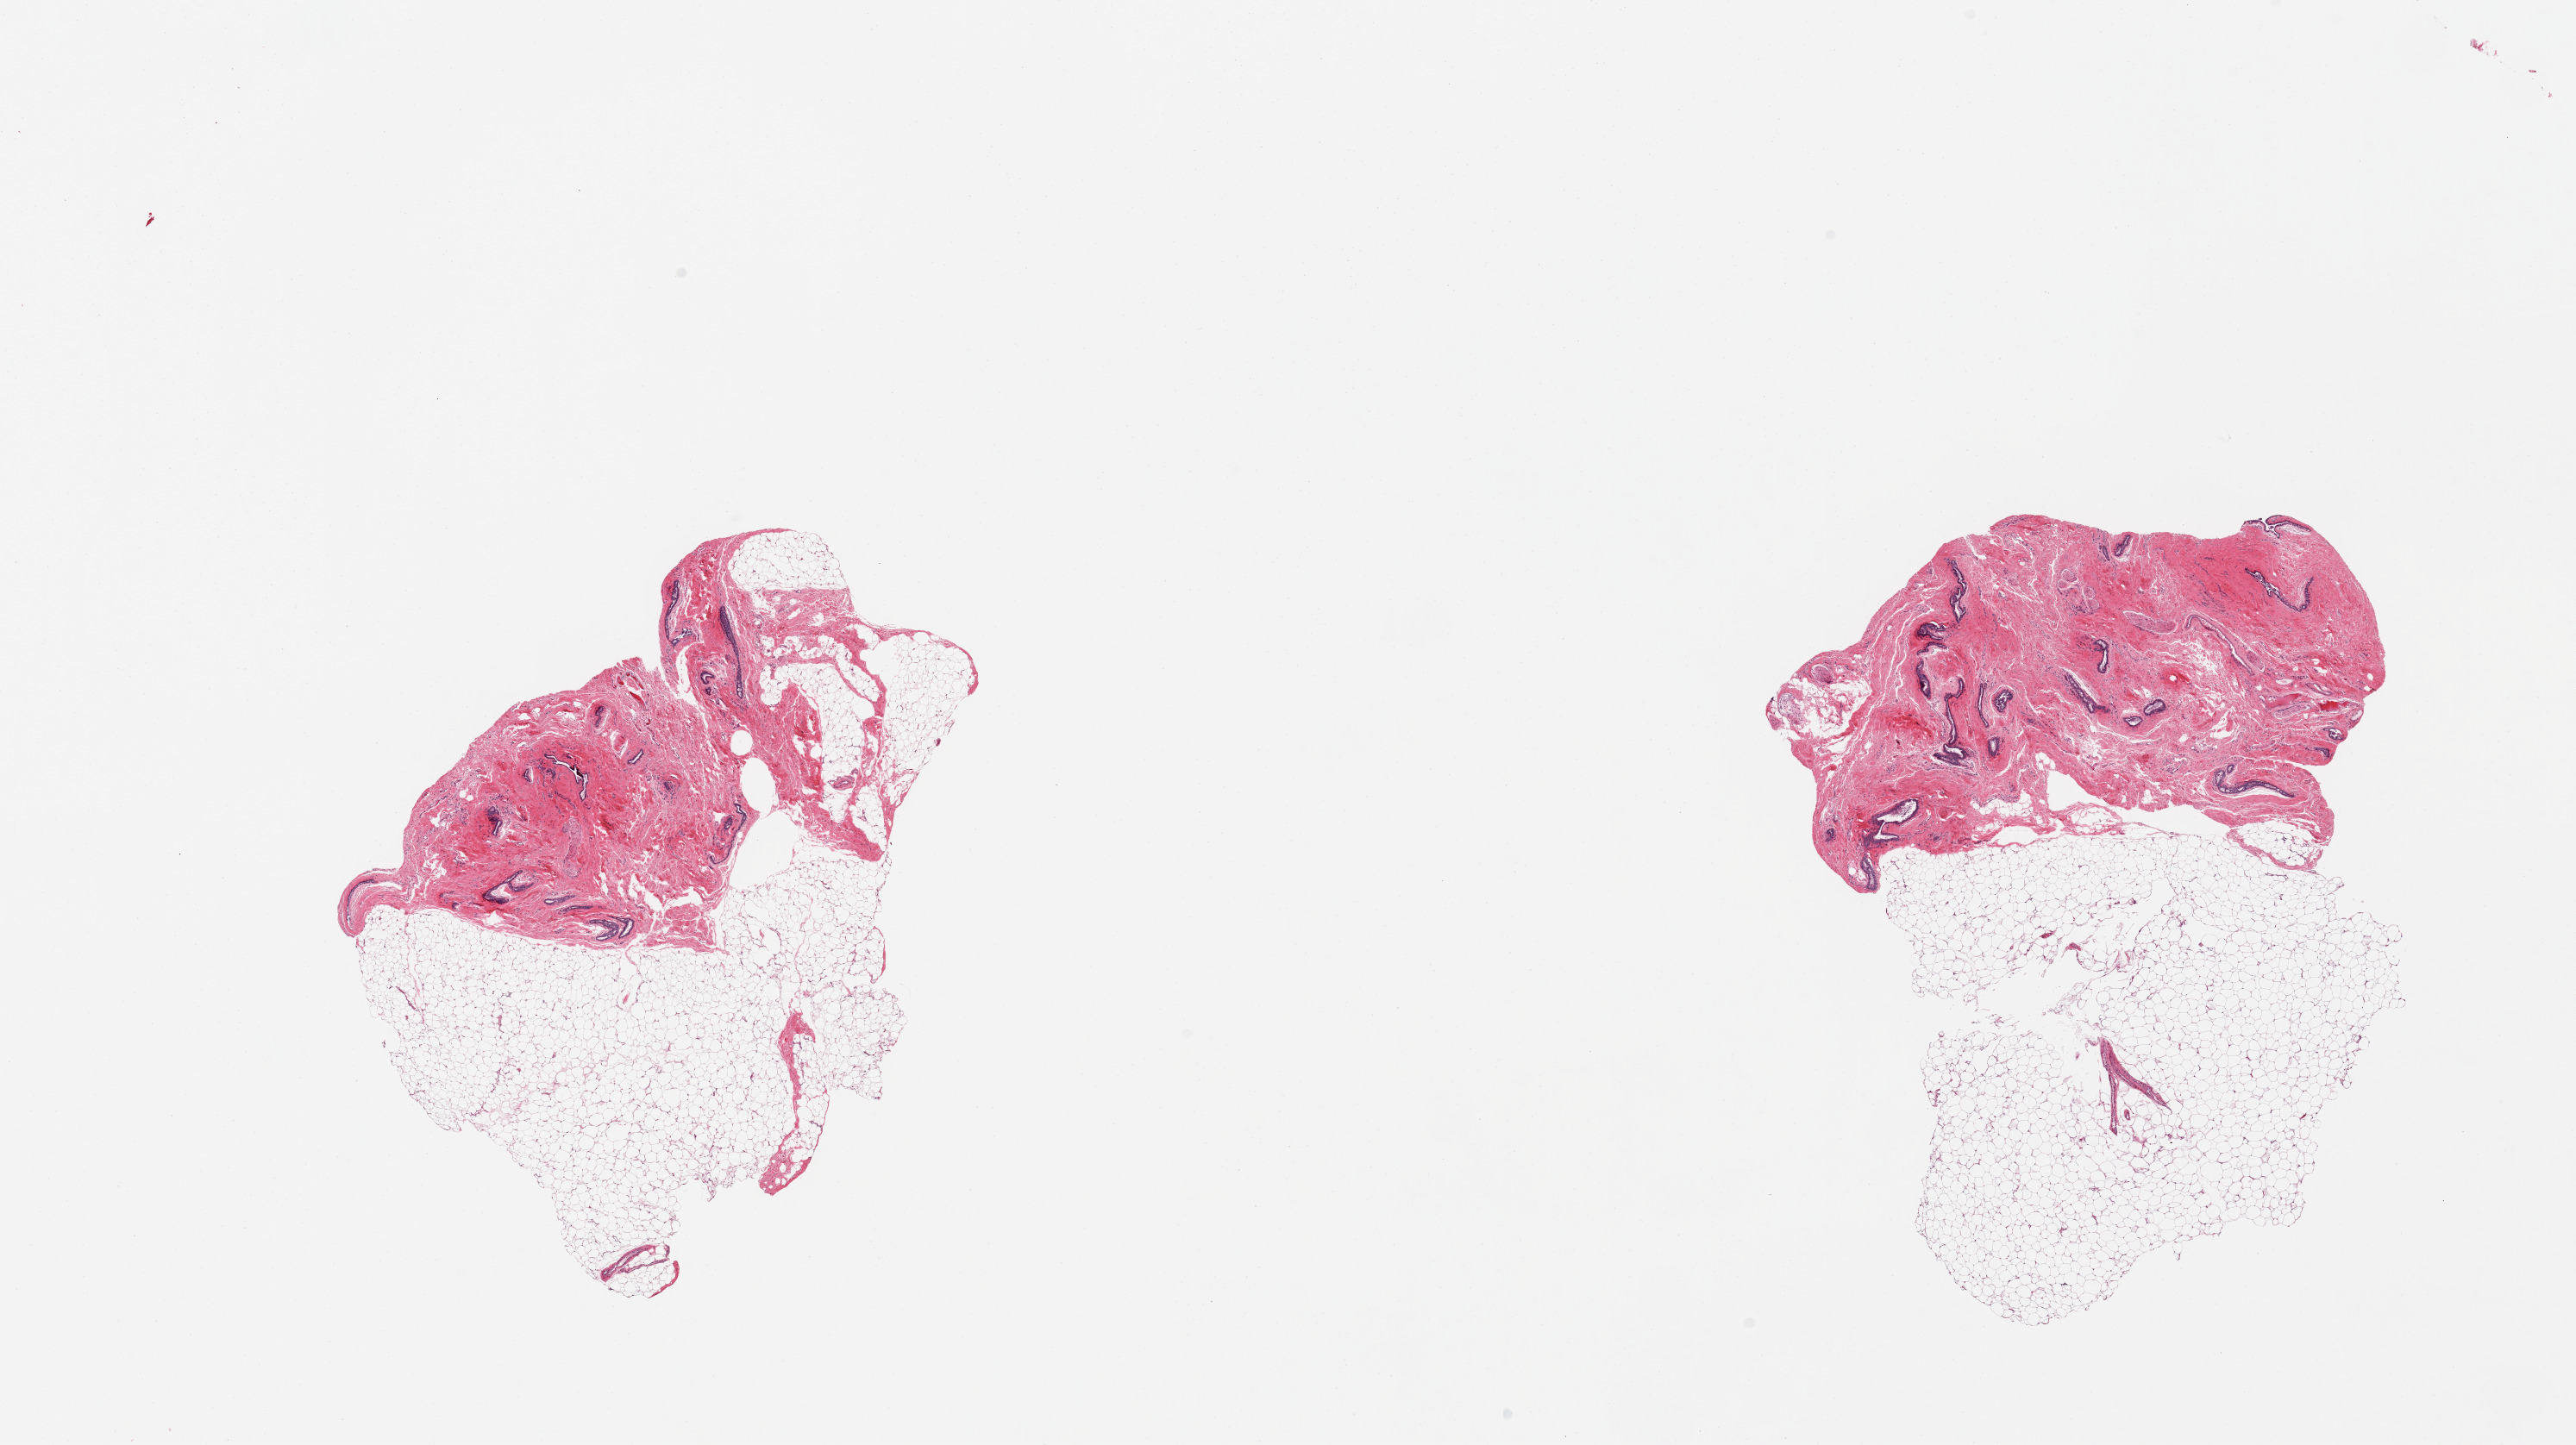
Digitized hematoxylin and eosin (H&E)-stained section — a low-resolution overview of the entire scanned area, about 23.6 x 13.3 mm, PAXgene-fixed paraffin-embedded (PFPE) section, sampled site (target tissue): breast, tissue donor sample. Male donor.
Reviewer comment on this tissue sample: 2 pieces; numerous ductal structures embedded in fibrotic stroma (gynecomastia) and over 50% external fat.